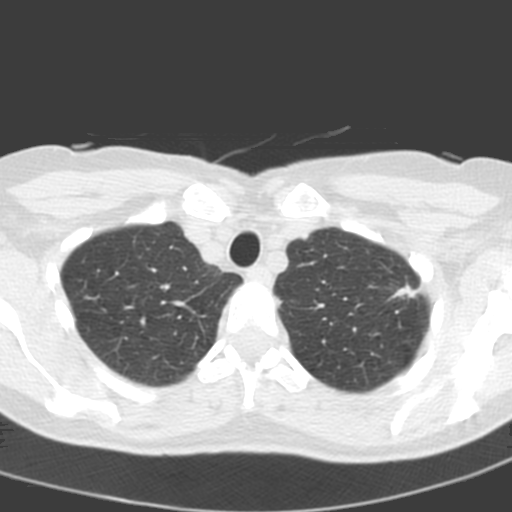
Chest CT (low-dose screening protocol), one axial image; baseline screening round; lung window (W 1500 / L -600 HU); slice 31 of 193 in the series; 512 × 512 image matrix. Female, age 58 years at enrolment. Current smoker at enrolment.
Expert-annotated lung lesion, bounding box [x1, y1, x2, y2] px = [379, 271, 426, 319]. Screening reader's record for this exam (one nodule recorded; not confirmed to be the boxed lesion): non-calcified nodule or mass ≥4 mm, left upper lobe, 14 × 10 mm, spiculated (stellate) margins, soft tissue attenuation.